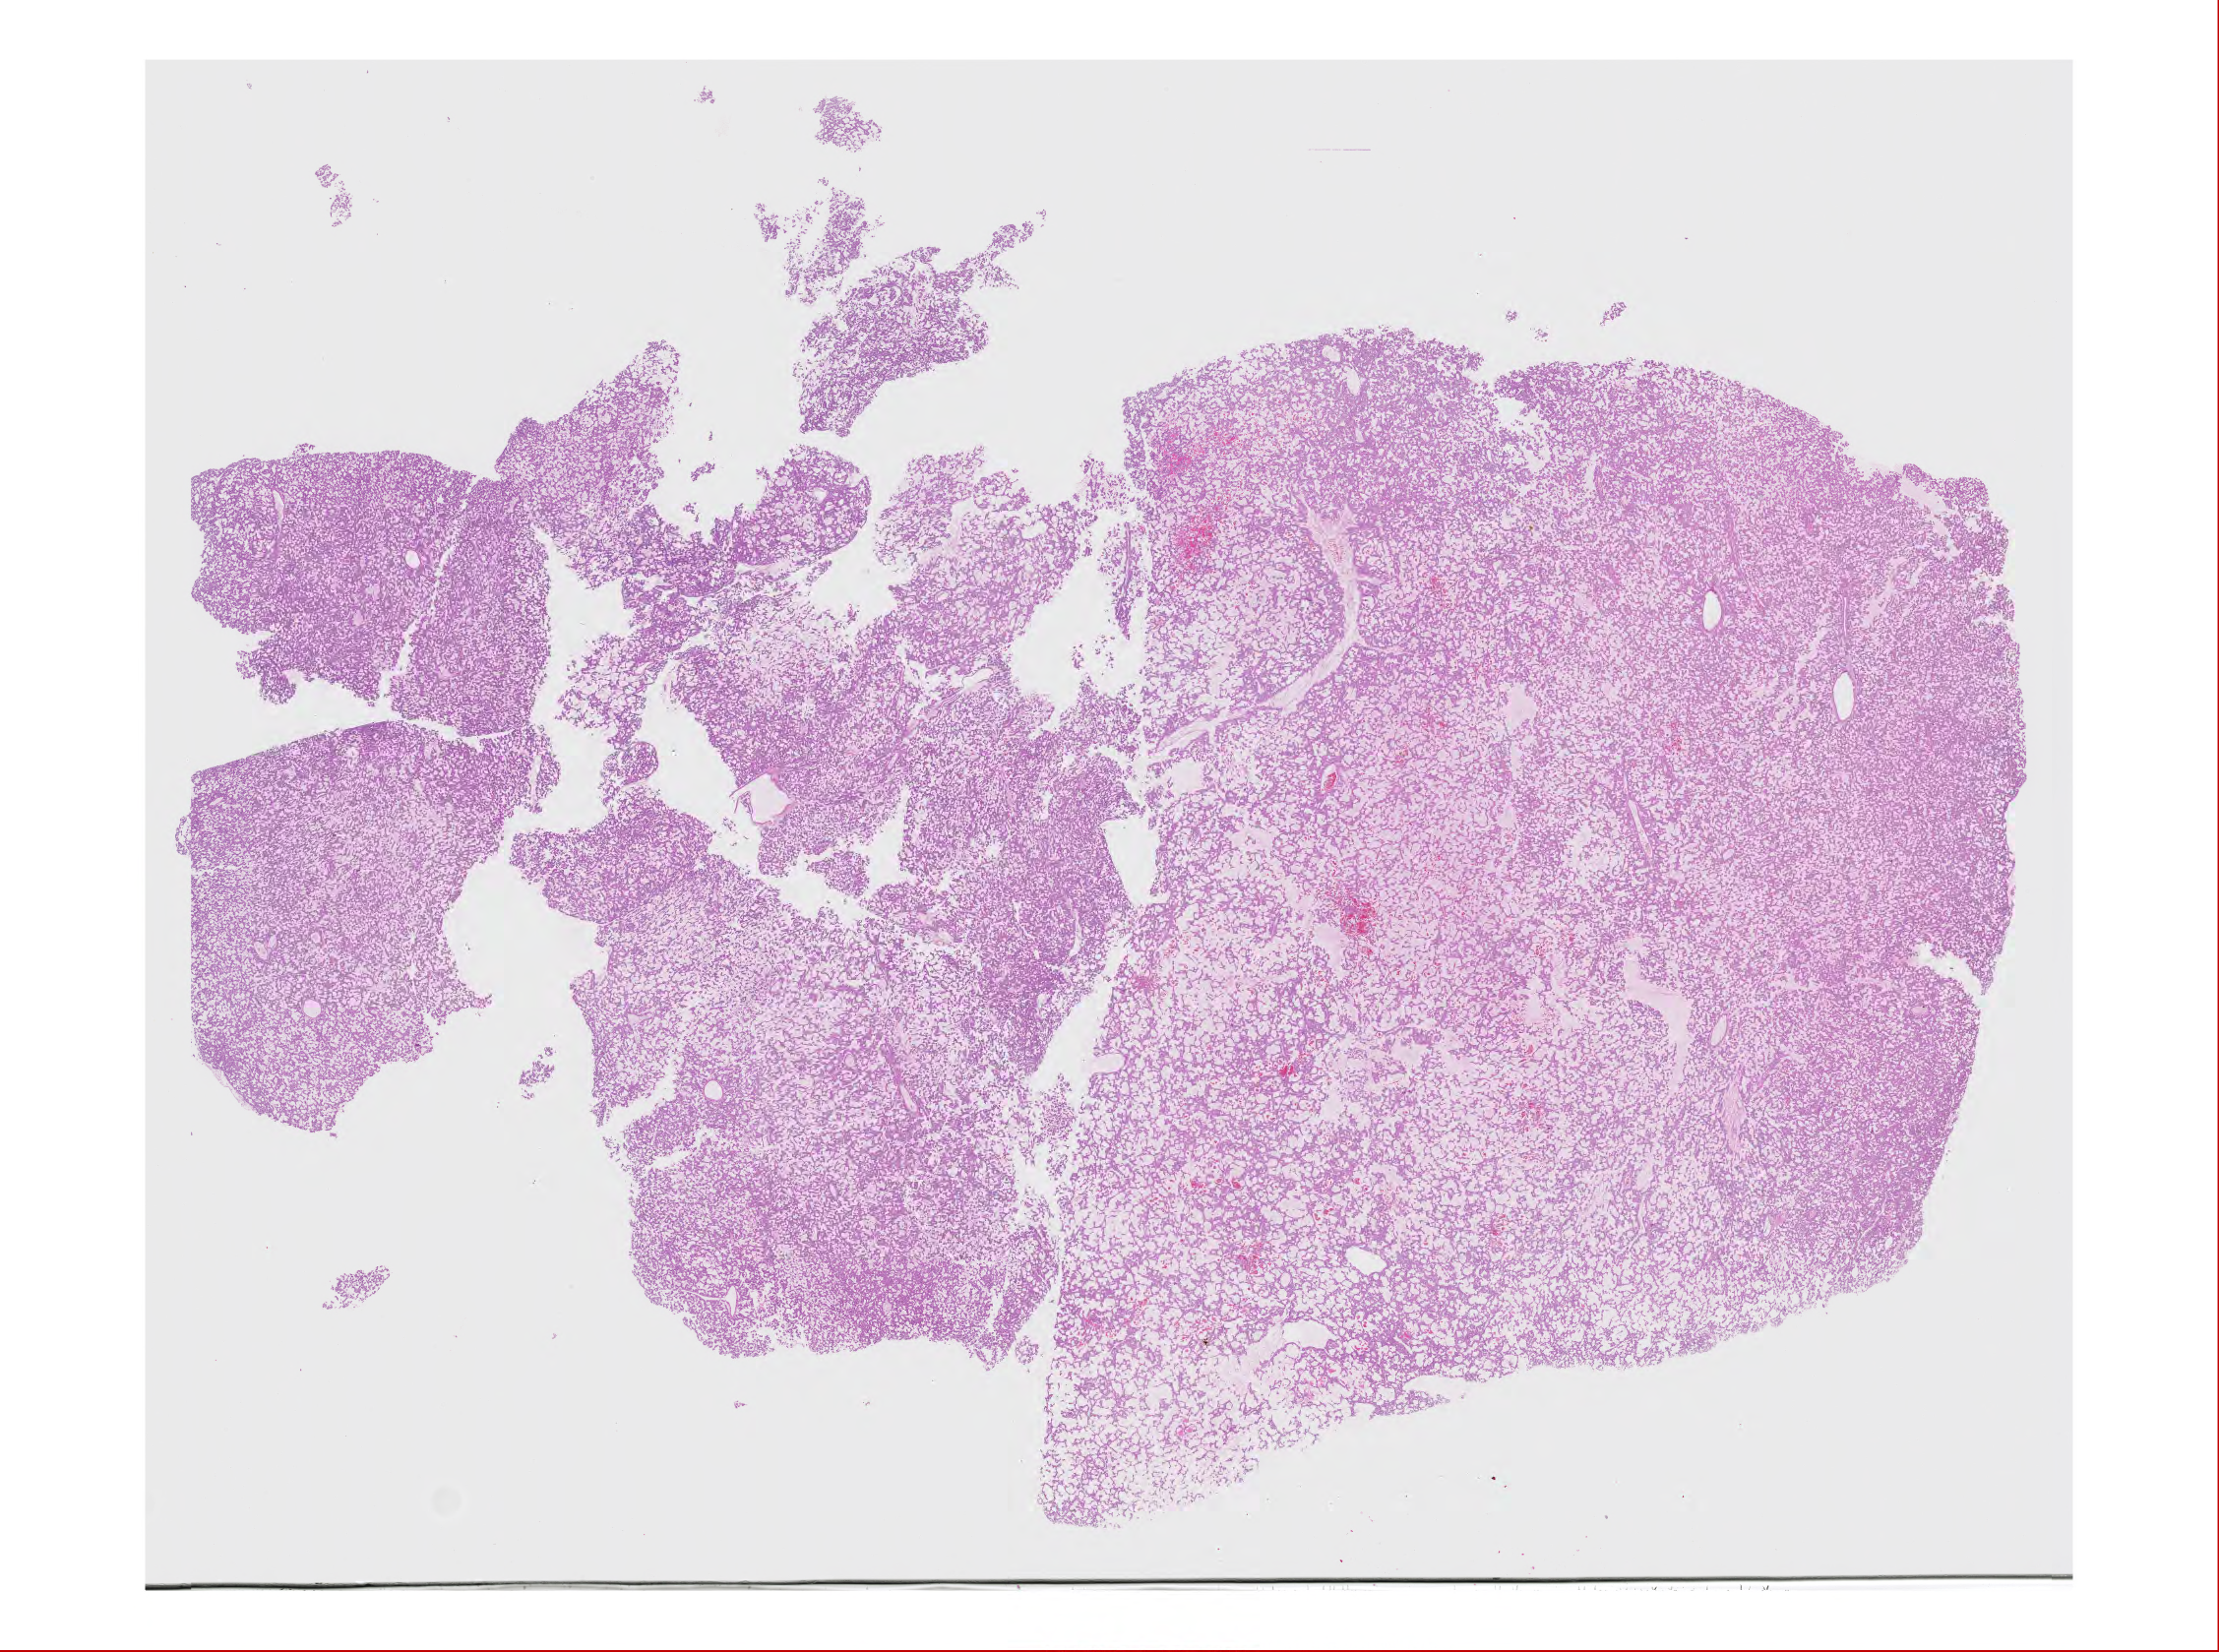
Digitized H&E-stained tissue section (whole slide), low-resolution overview of the scanned area, about 36.1 x 26.9 mm (slide scanned at 20x); formalin-fixed paraffin-embedded (FFPE) diagnostic section; liver, primary tumour sample. Female, age 65 years at initial diagnosis. Histologic grade: G1 (well differentiated).
- AJCC pathologic stage: IIIA (7th edition)
- TNM: T3a N0 M0
- diagnosis: Hepatocellular carcinoma, NOS